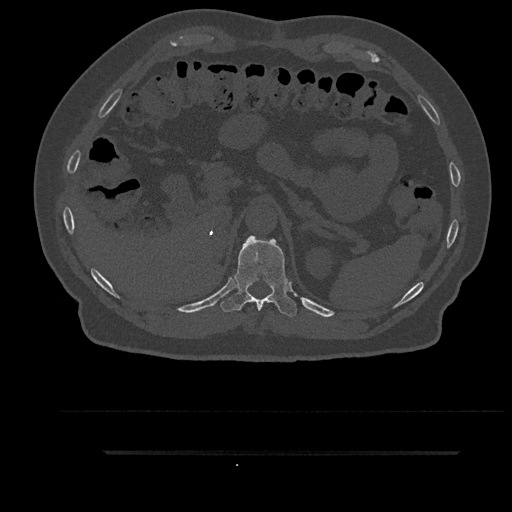
CT including the spine, one axial slice. Slice 310 of 797 in the series (ordered by position). Bone window (W 1800 / L 400 HU). 0.5 mm slice thickness. 512 × 512 image matrix, field of view 432 × 432 mm. Male patient, age 63 years. From the clinical record (not read from this slice): primary cancer: renal; vertebrae with lytic lesions (as recorded): T8.
Structures marked on this image (semi-automatic segmentation, software-assisted and operator-edited):
- T11 vertebra: bounding box <221,235,297,317> (left, top, right, bottom; pixels)